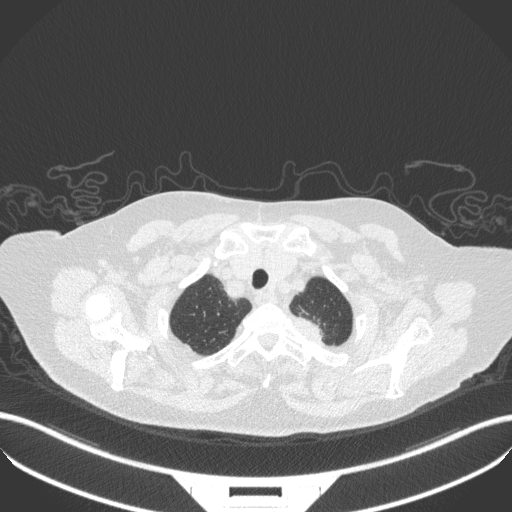
Chest CT, one axial slice. Position 311 of 353 along the scan axis. Reconstruction kernel B31f. 100 kVp. Lung window (W 1500 / L -600 HU). 512 × 512 image matrix, field of view 400 × 400 mm. Female patient, age 81 years. Case-level facts recorded for this patient, not image findings: clinical TNM (as recorded): T2a N0 M0.
Structures marked on this image (rectangle marked by the reading radiologist):
- lung tumour (recorded histology: adenocarcinoma): bounding box [x1, y1, x2, y2] px = [295, 309, 334, 356]